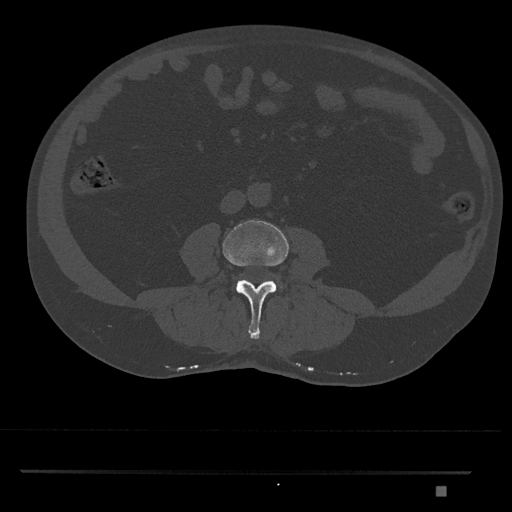
CT including the spine, one axial slice; slice 666 of 1134 in the series (ordered by position); 120 kVp; bone window (W 1800 / L 400 HU); 0.5 mm slice thickness; 512 × 512 image matrix. Patient: male, 65 years. Case-level facts recorded for this patient, not image findings: primary cancer: prostate.
Annotated regions visible in this slice (semi-automatic segmentation, software-assisted and operator-edited):
- L3 vertebra: bounding box [x1, y1, x2, y2] px = [223, 220, 289, 339]
- L4 vertebra: [277, 280, 279, 283]